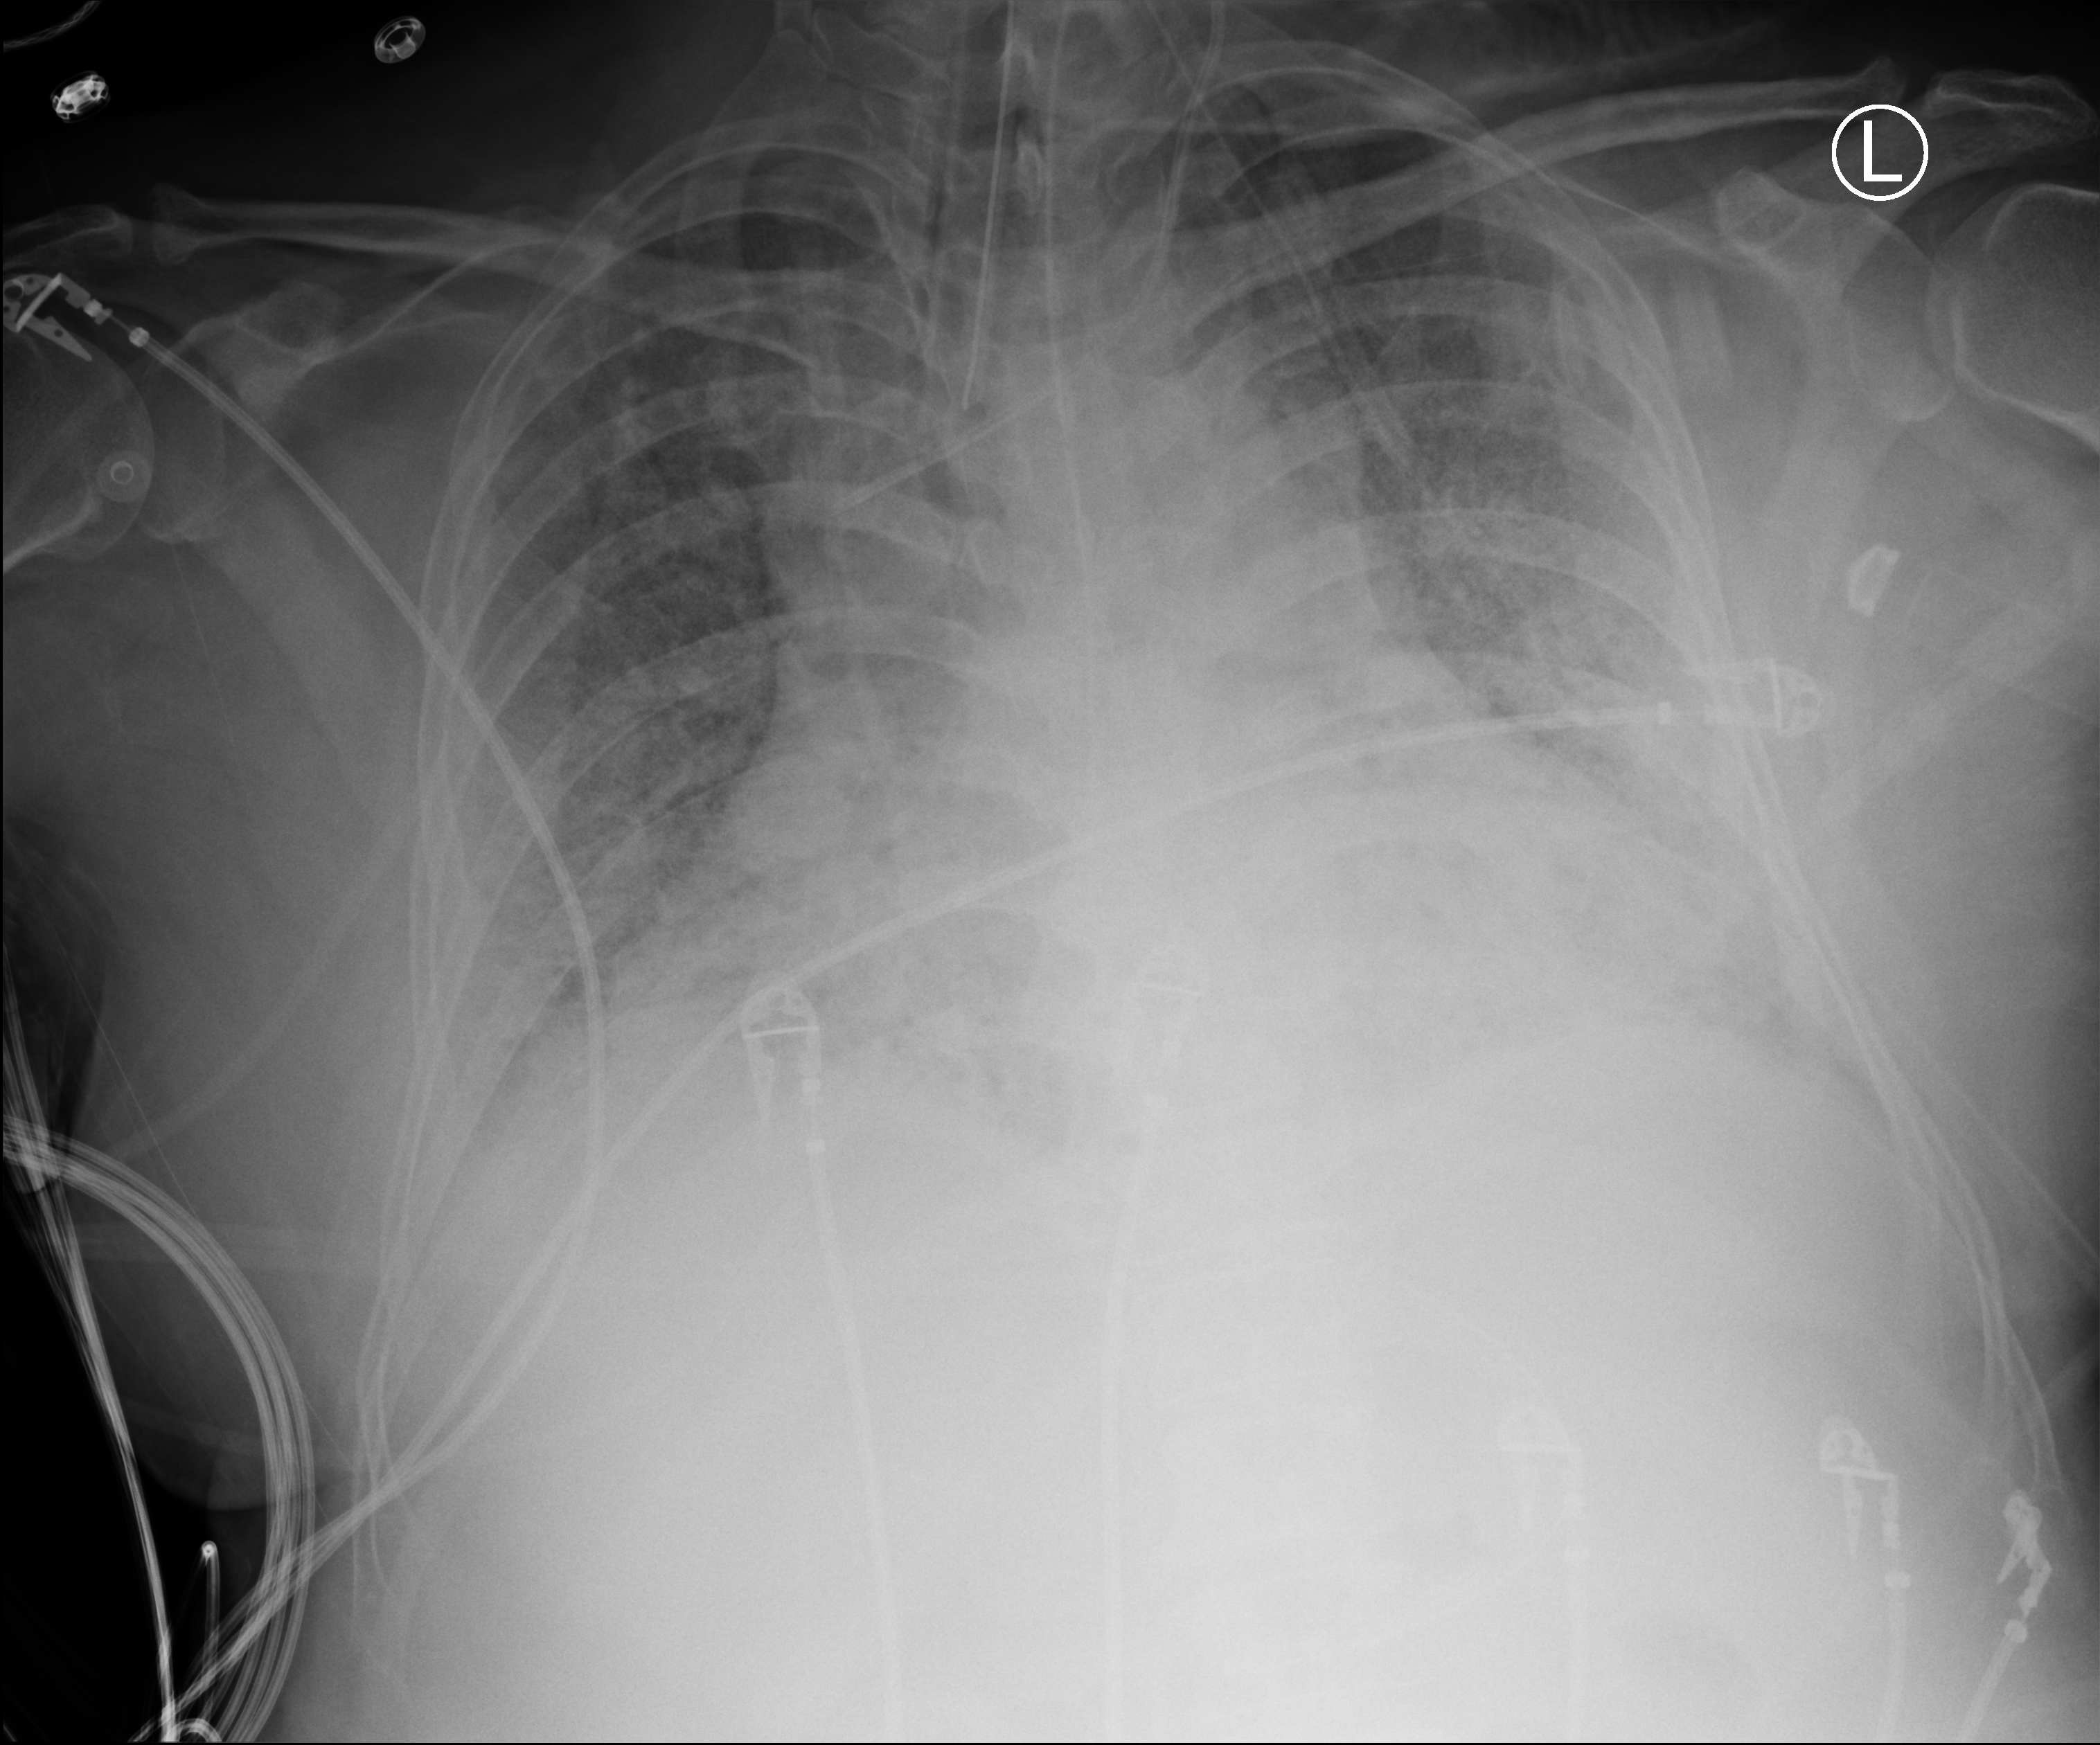
Bedside chest radiograph (computed radiography); anteroposterior (AP) projection. Patient hospitalised with COVID-19, aged 18–59 years.
Hospital-stay facts (about this admission, not read from this image; timing relative to this image not recorded):
- admitted to intensive care during this hospital stay: yes
- hypertension (admission record): no